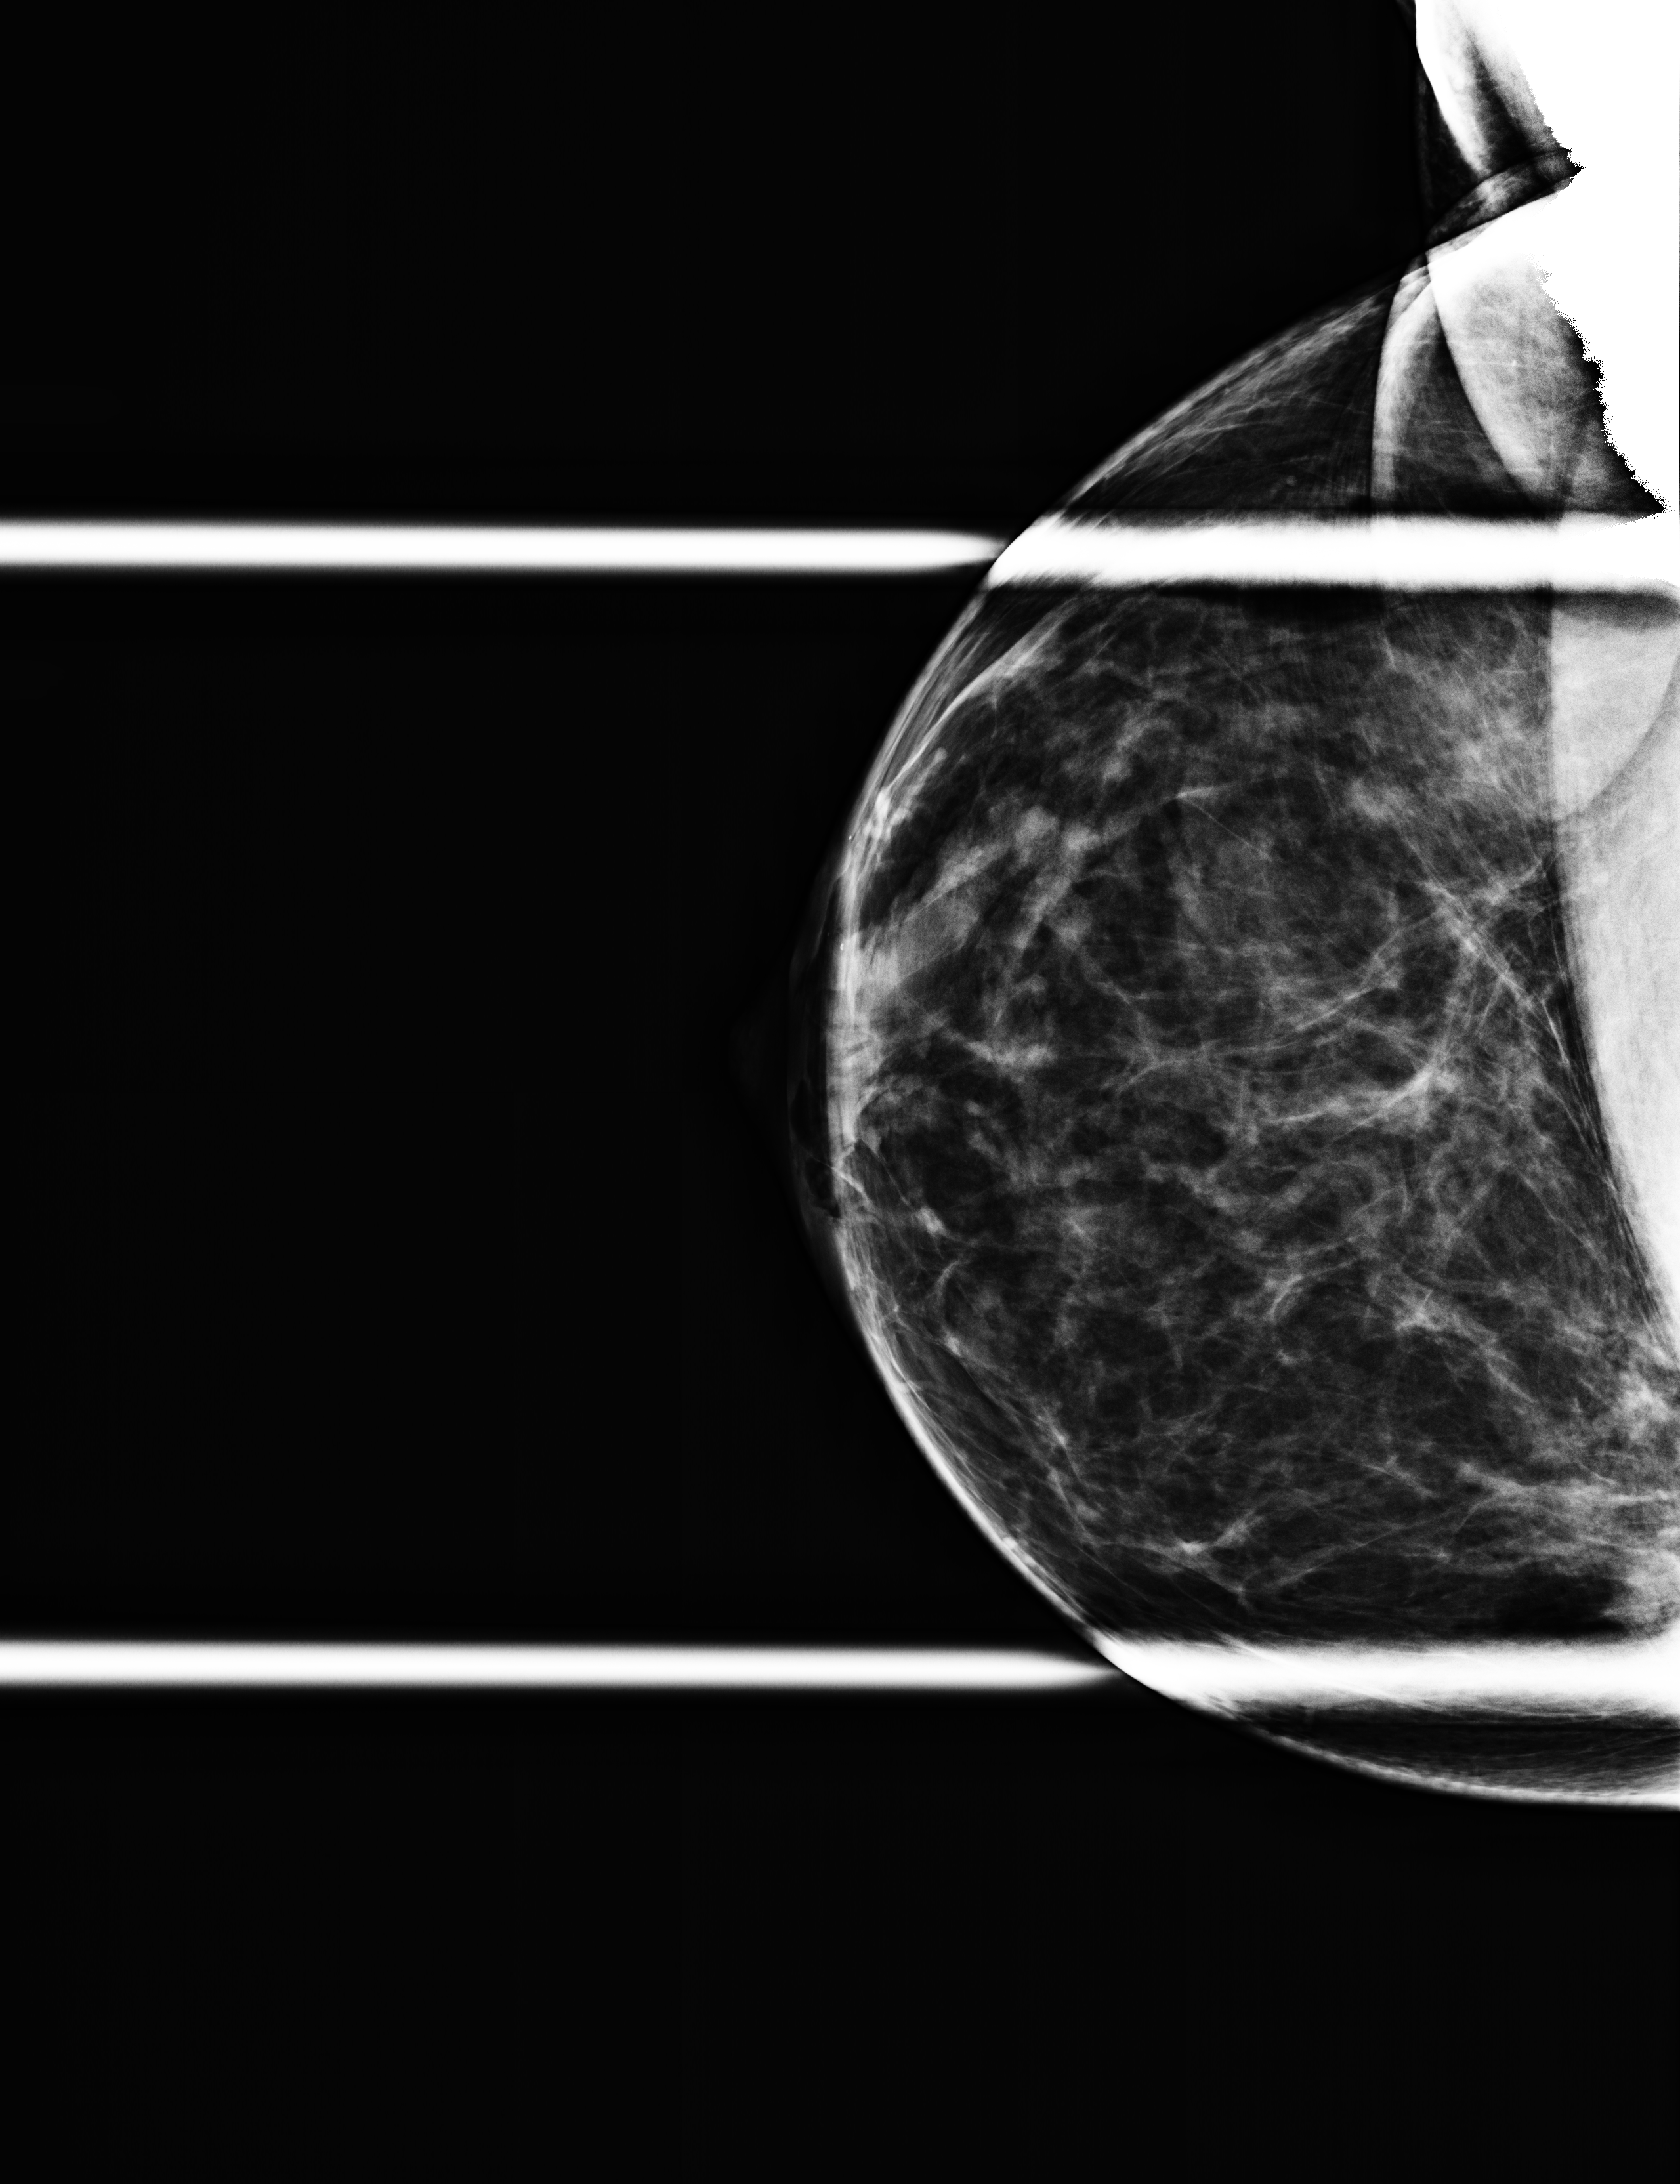
Additional work-up view. Patient aged 45 years (female).
Image type: full-field digital mammogram. Breast: right. Projection: CC view, spot compression.